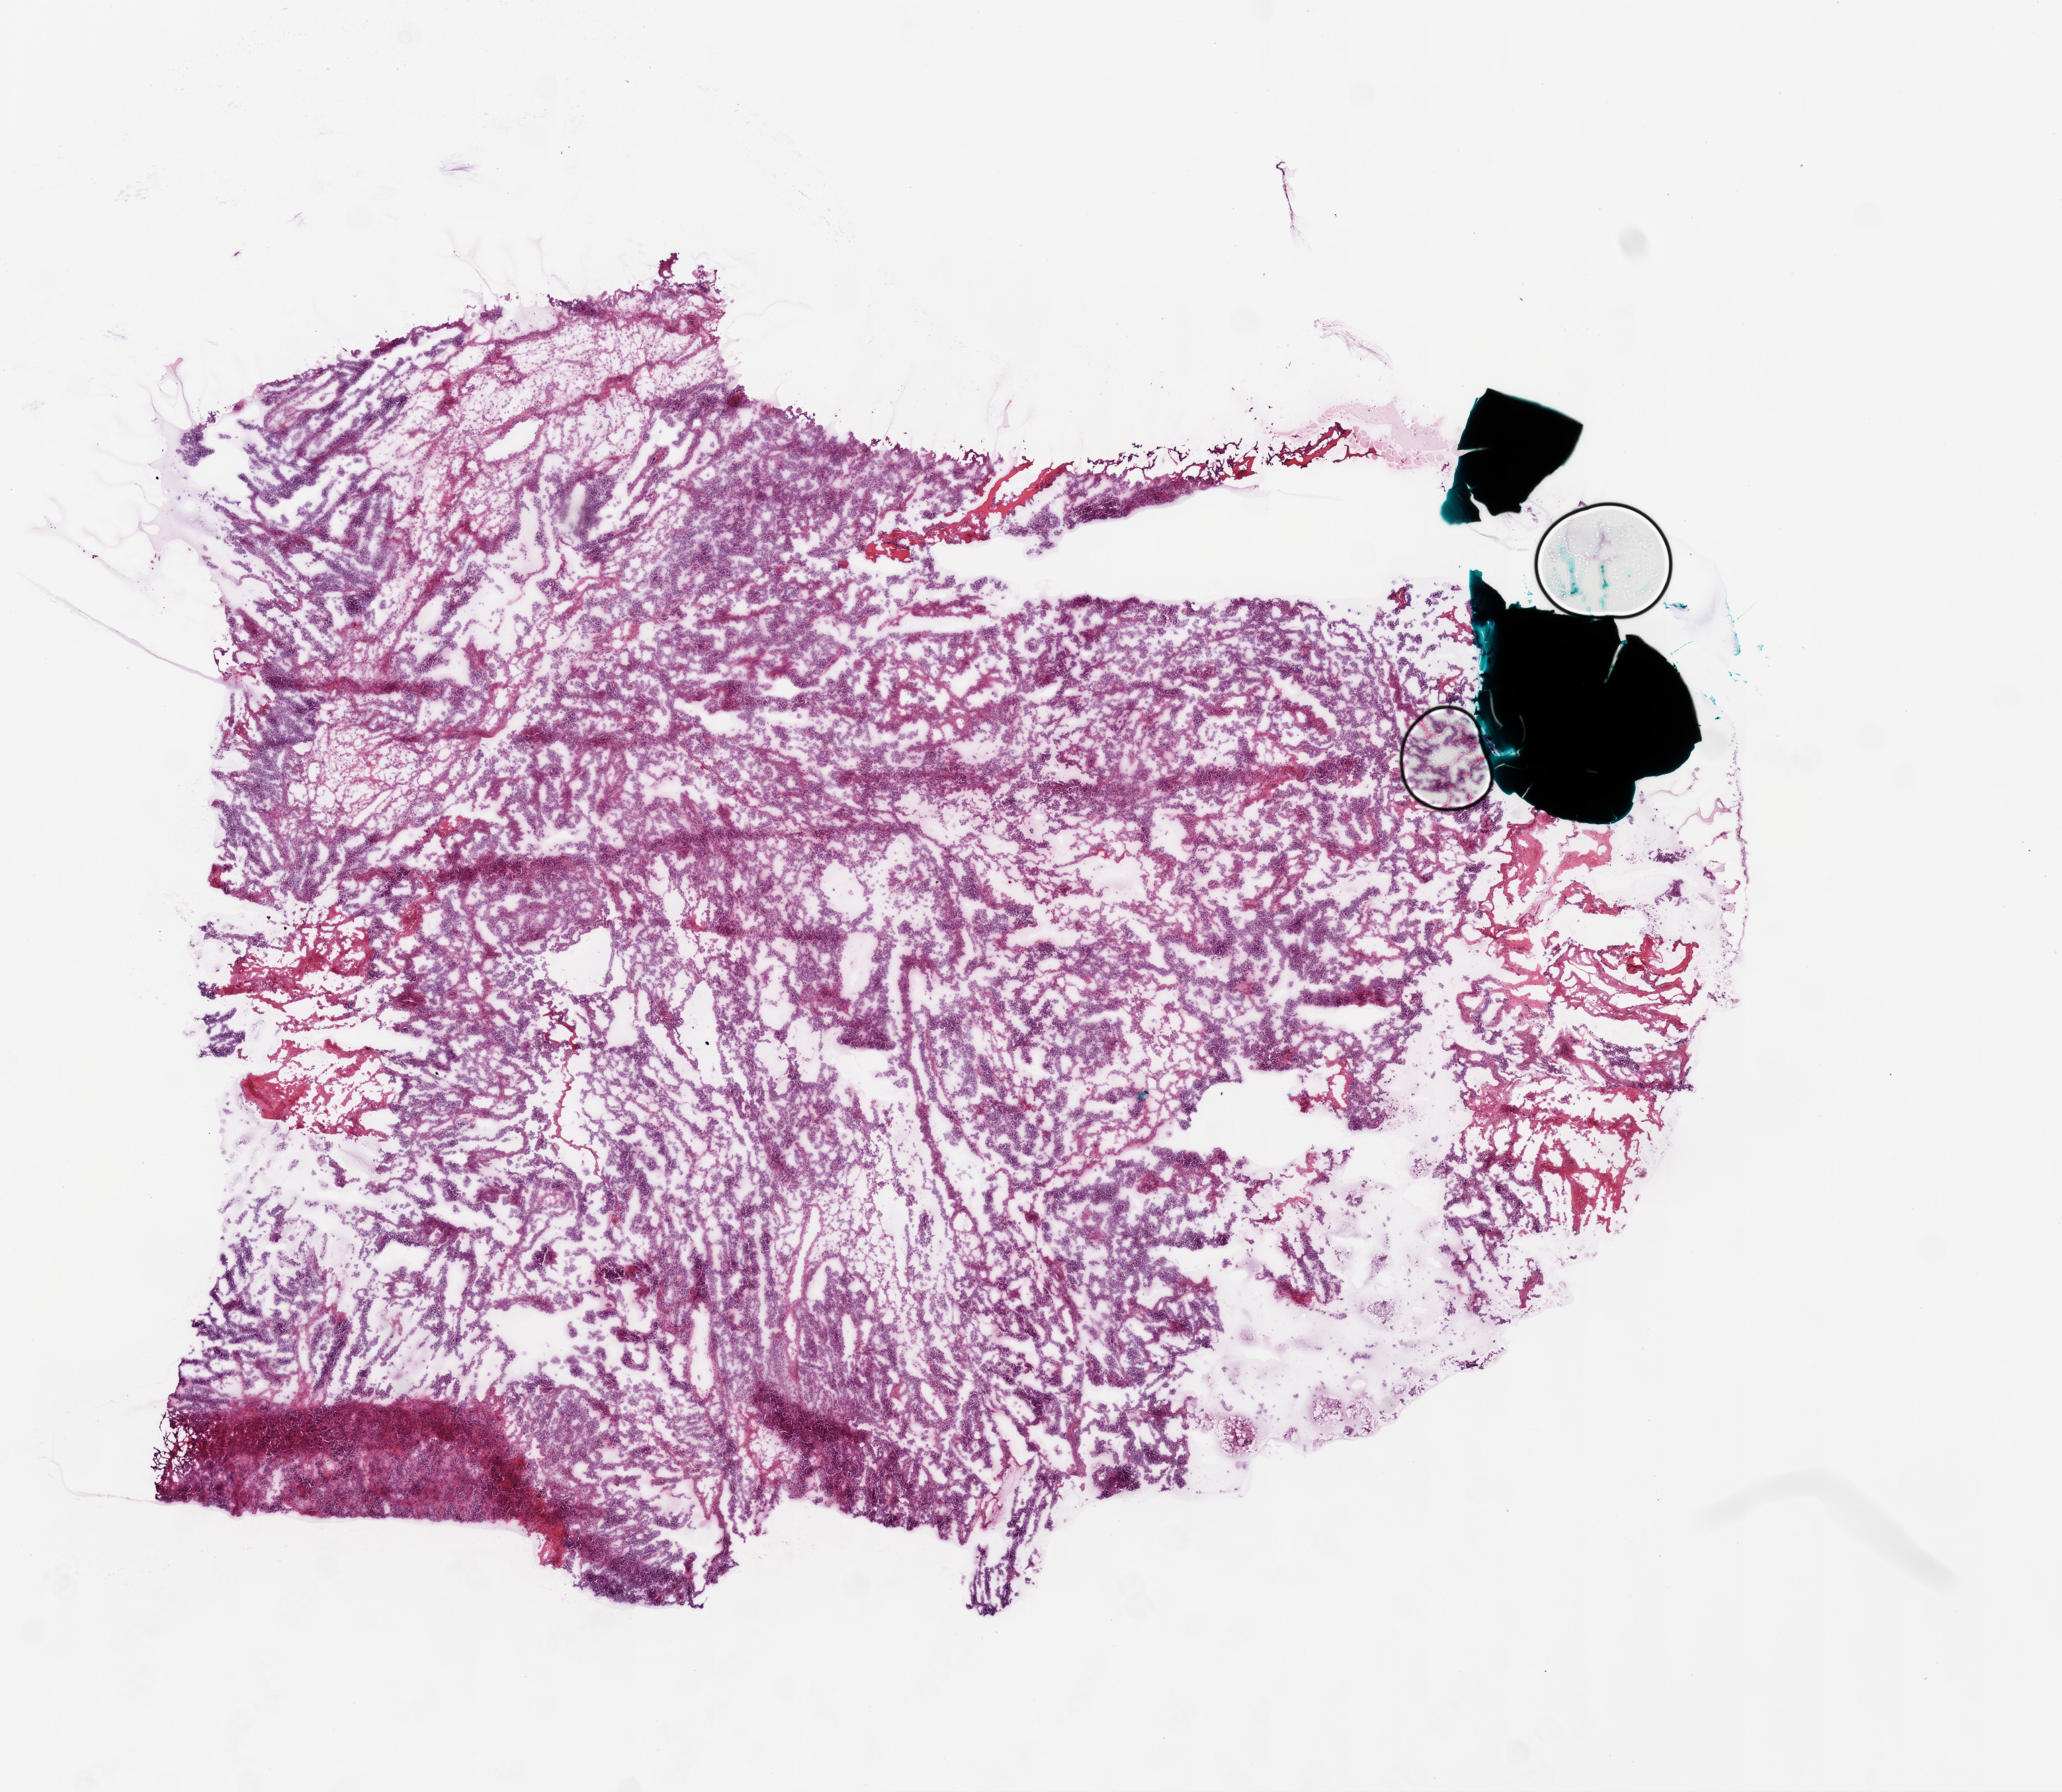
Hematoxylin and eosin (H&E) stained whole-slide image — low-resolution overview of the scanned area, about 12.6 x 10.9 mm (from a 20x scan), frozen section from the bottom of the tissue portion, sample: primary tumour, ovary. Patient: female, age at initial diagnosis 77 years. Histologic grade: G3 (poorly differentiated). Slide review estimates, as recorded: tumour cells 85%, tumour nuclei 90%, normal cells 5%, stromal cells 10%, necrosis 0%.
- FIGO stage: IIIC
- pathologic diagnosis: Serous cystadenocarcinoma, NOS